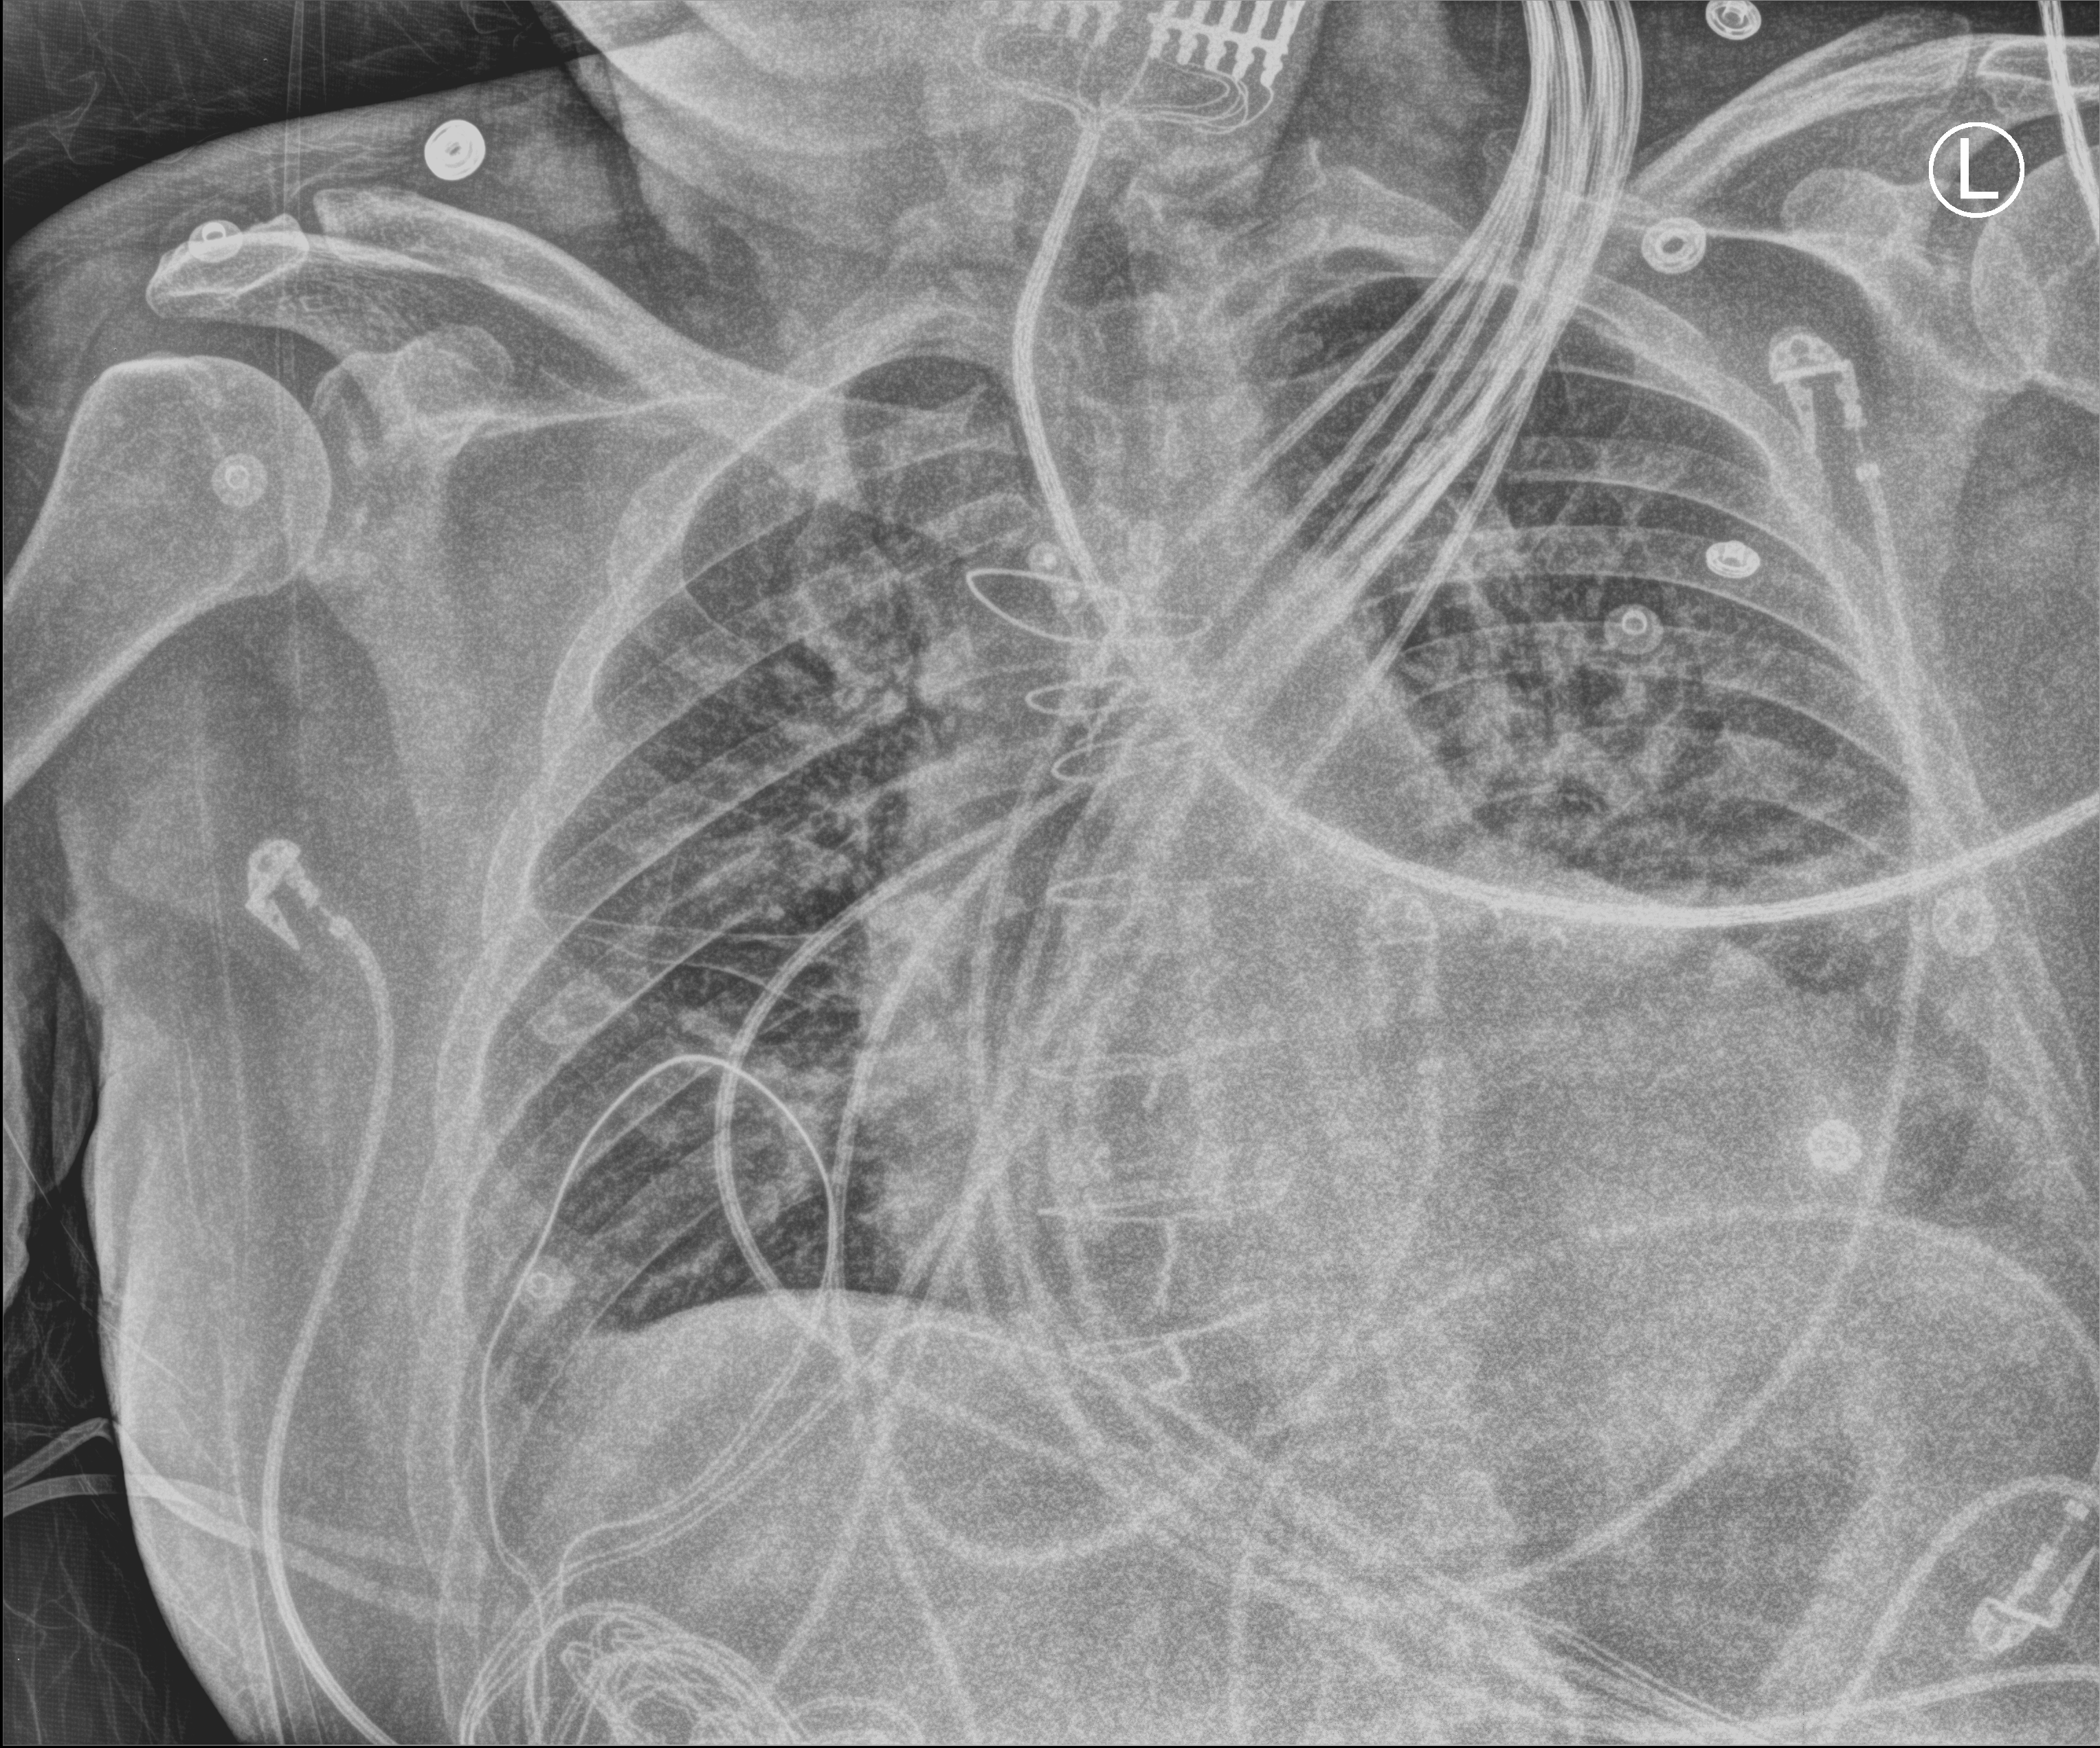
Chest X-ray (portable), anteroposterior (AP) projection. Patient hospitalised with COVID-19; male, aged 18–59 years.
Hospital-stay facts (about this admission, not read from this image; timing relative to this image not recorded):
- mechanically ventilated during this hospital stay: no